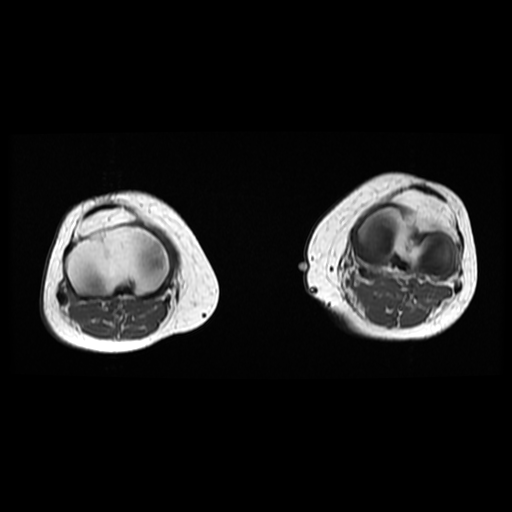
MRI of an extremity soft-tissue mass, one axial slice; slice 26 of 38 in the series (ordered by position); 6 mm slice thickness; 512 × 512 image matrix, field of view 330 × 330 mm. Female patient. Case-level facts recorded for this patient, not image findings: histological type: extraskeletal high grade osteogenic sarcoma; grade: high; site of the primary tumour: left calf.
Annotated regions visible in this slice (manually delineated by an expert):
- gross tumour volume (mass): bounding box [x1, y1, x2, y2] px = [356, 282, 375, 301]